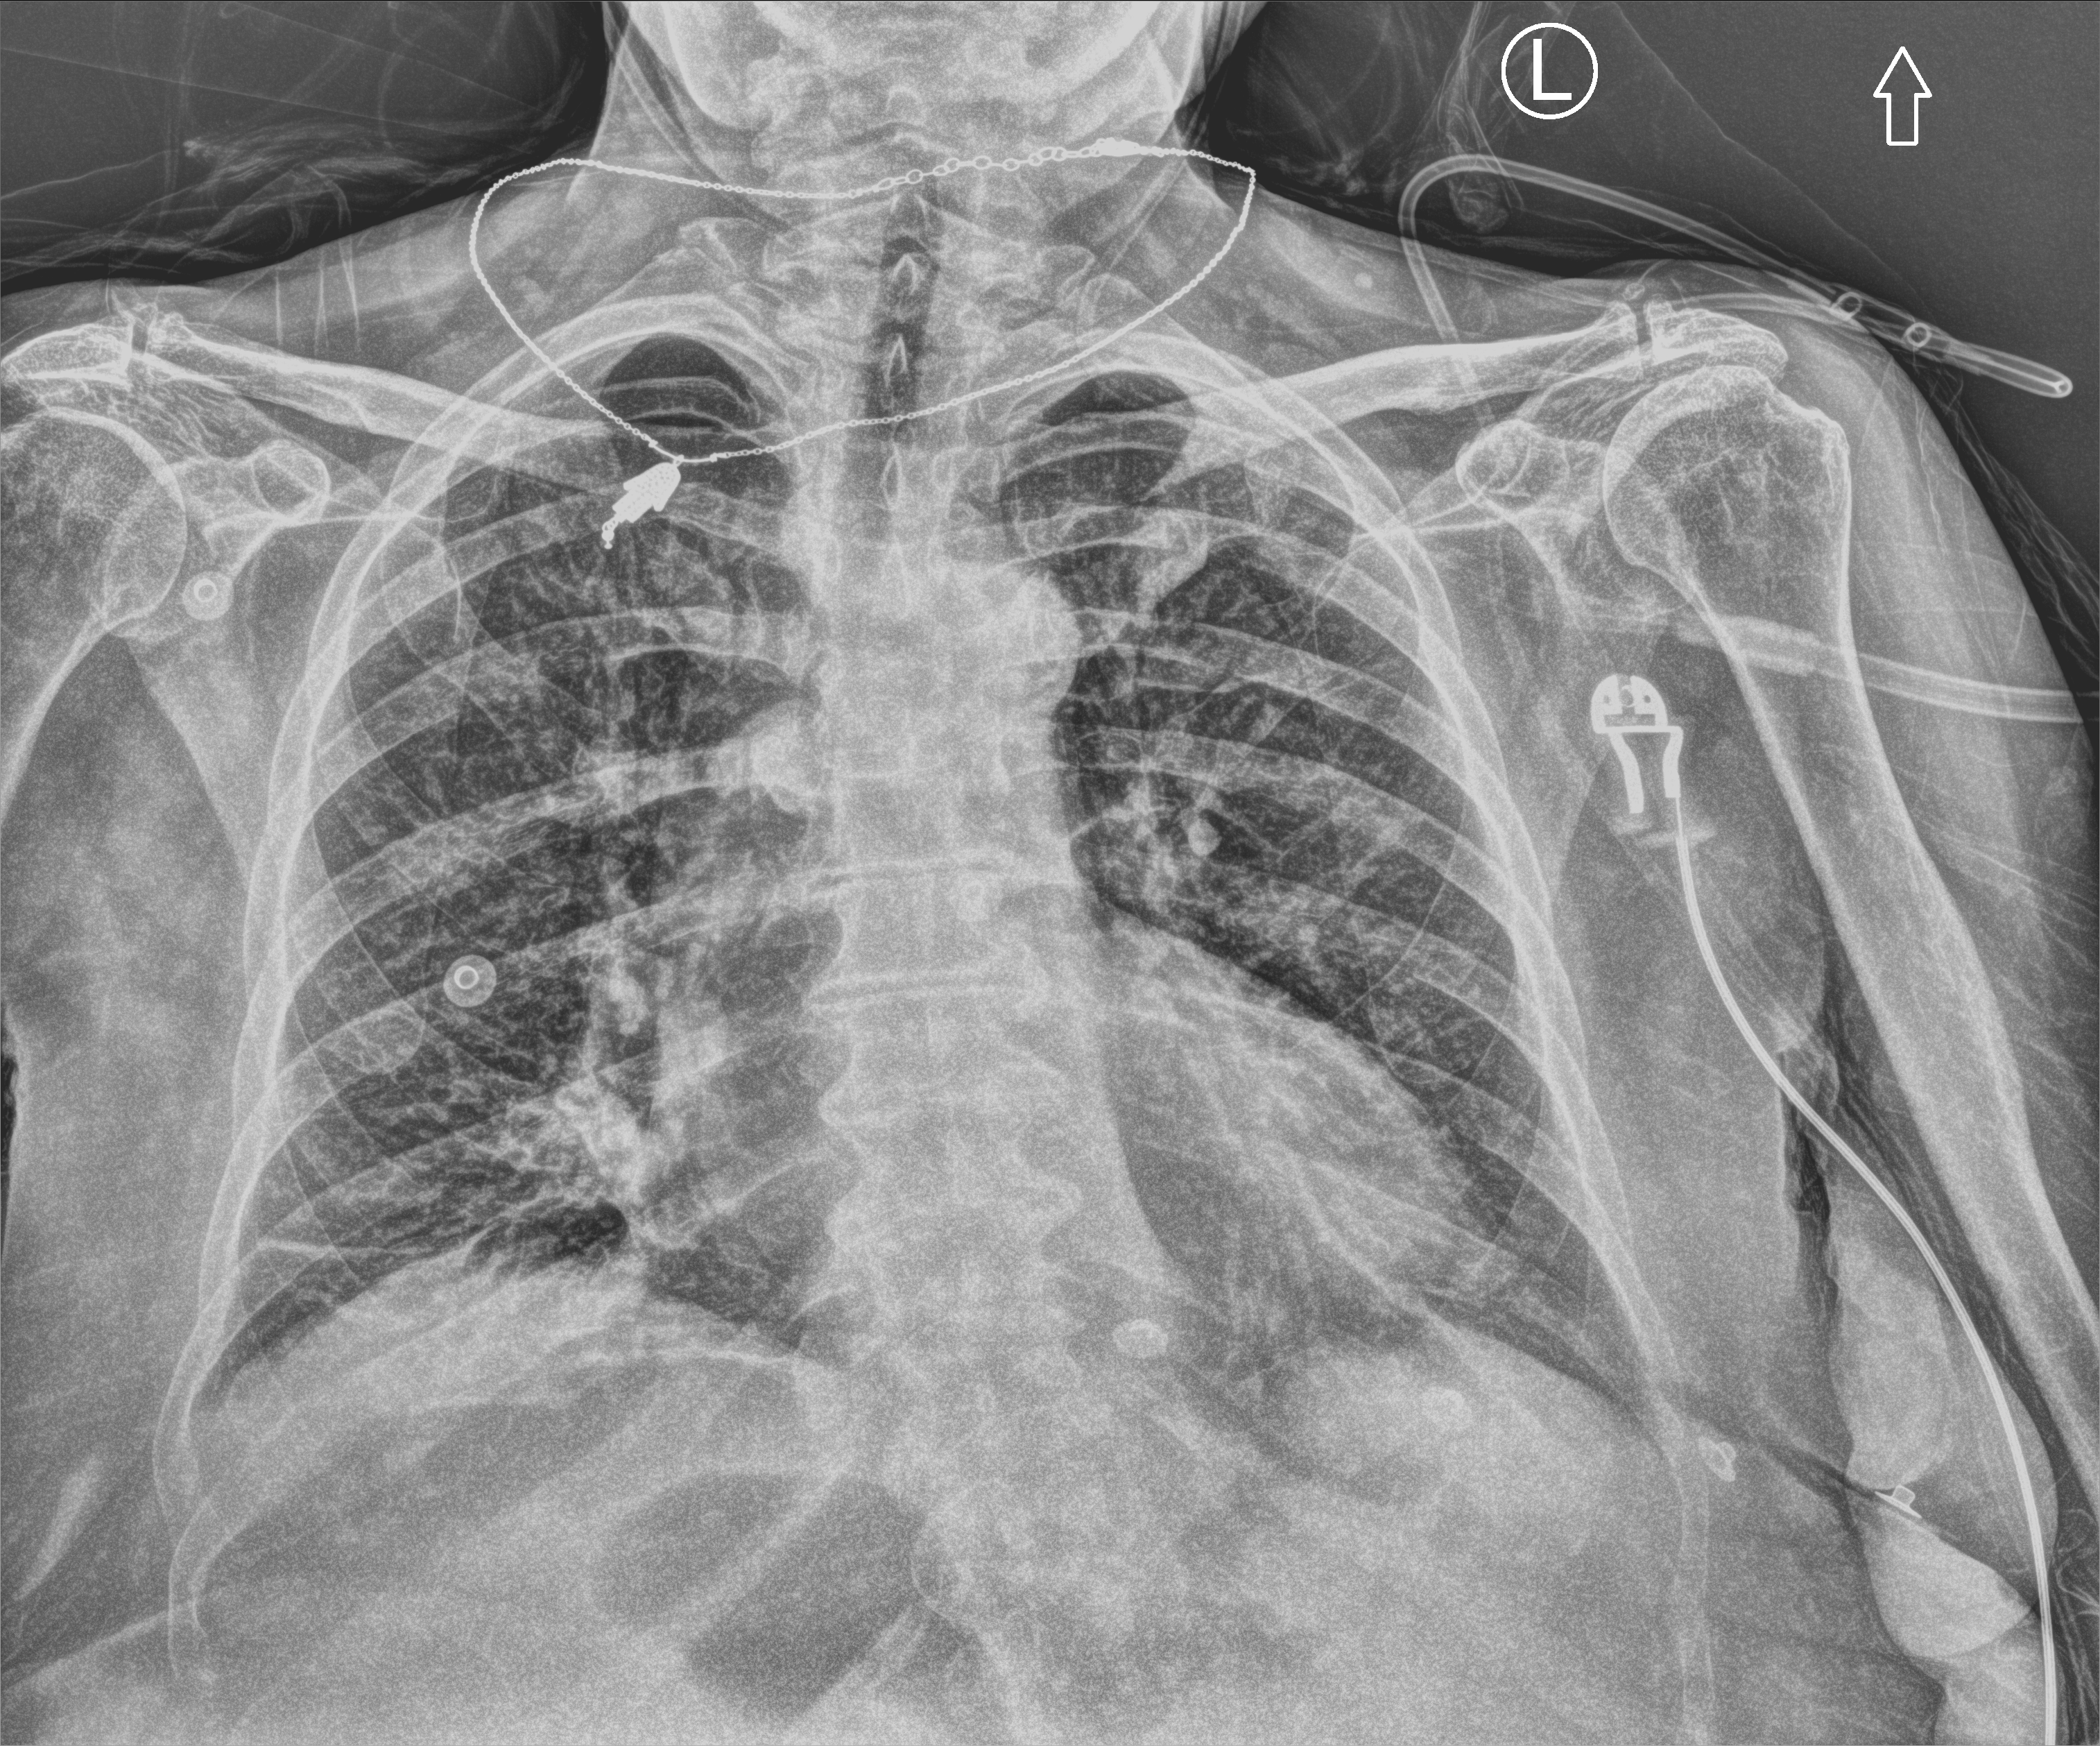
Chest X-ray (portable), anteroposterior (AP) projection. Female patient hospitalised with COVID-19, age 60–74 years.
From the hospital-stay record, not from the radiograph (when in the stay this image was taken is not recorded): admitted to intensive care during this hospital stay: yes; mechanically ventilated during this hospital stay: no.